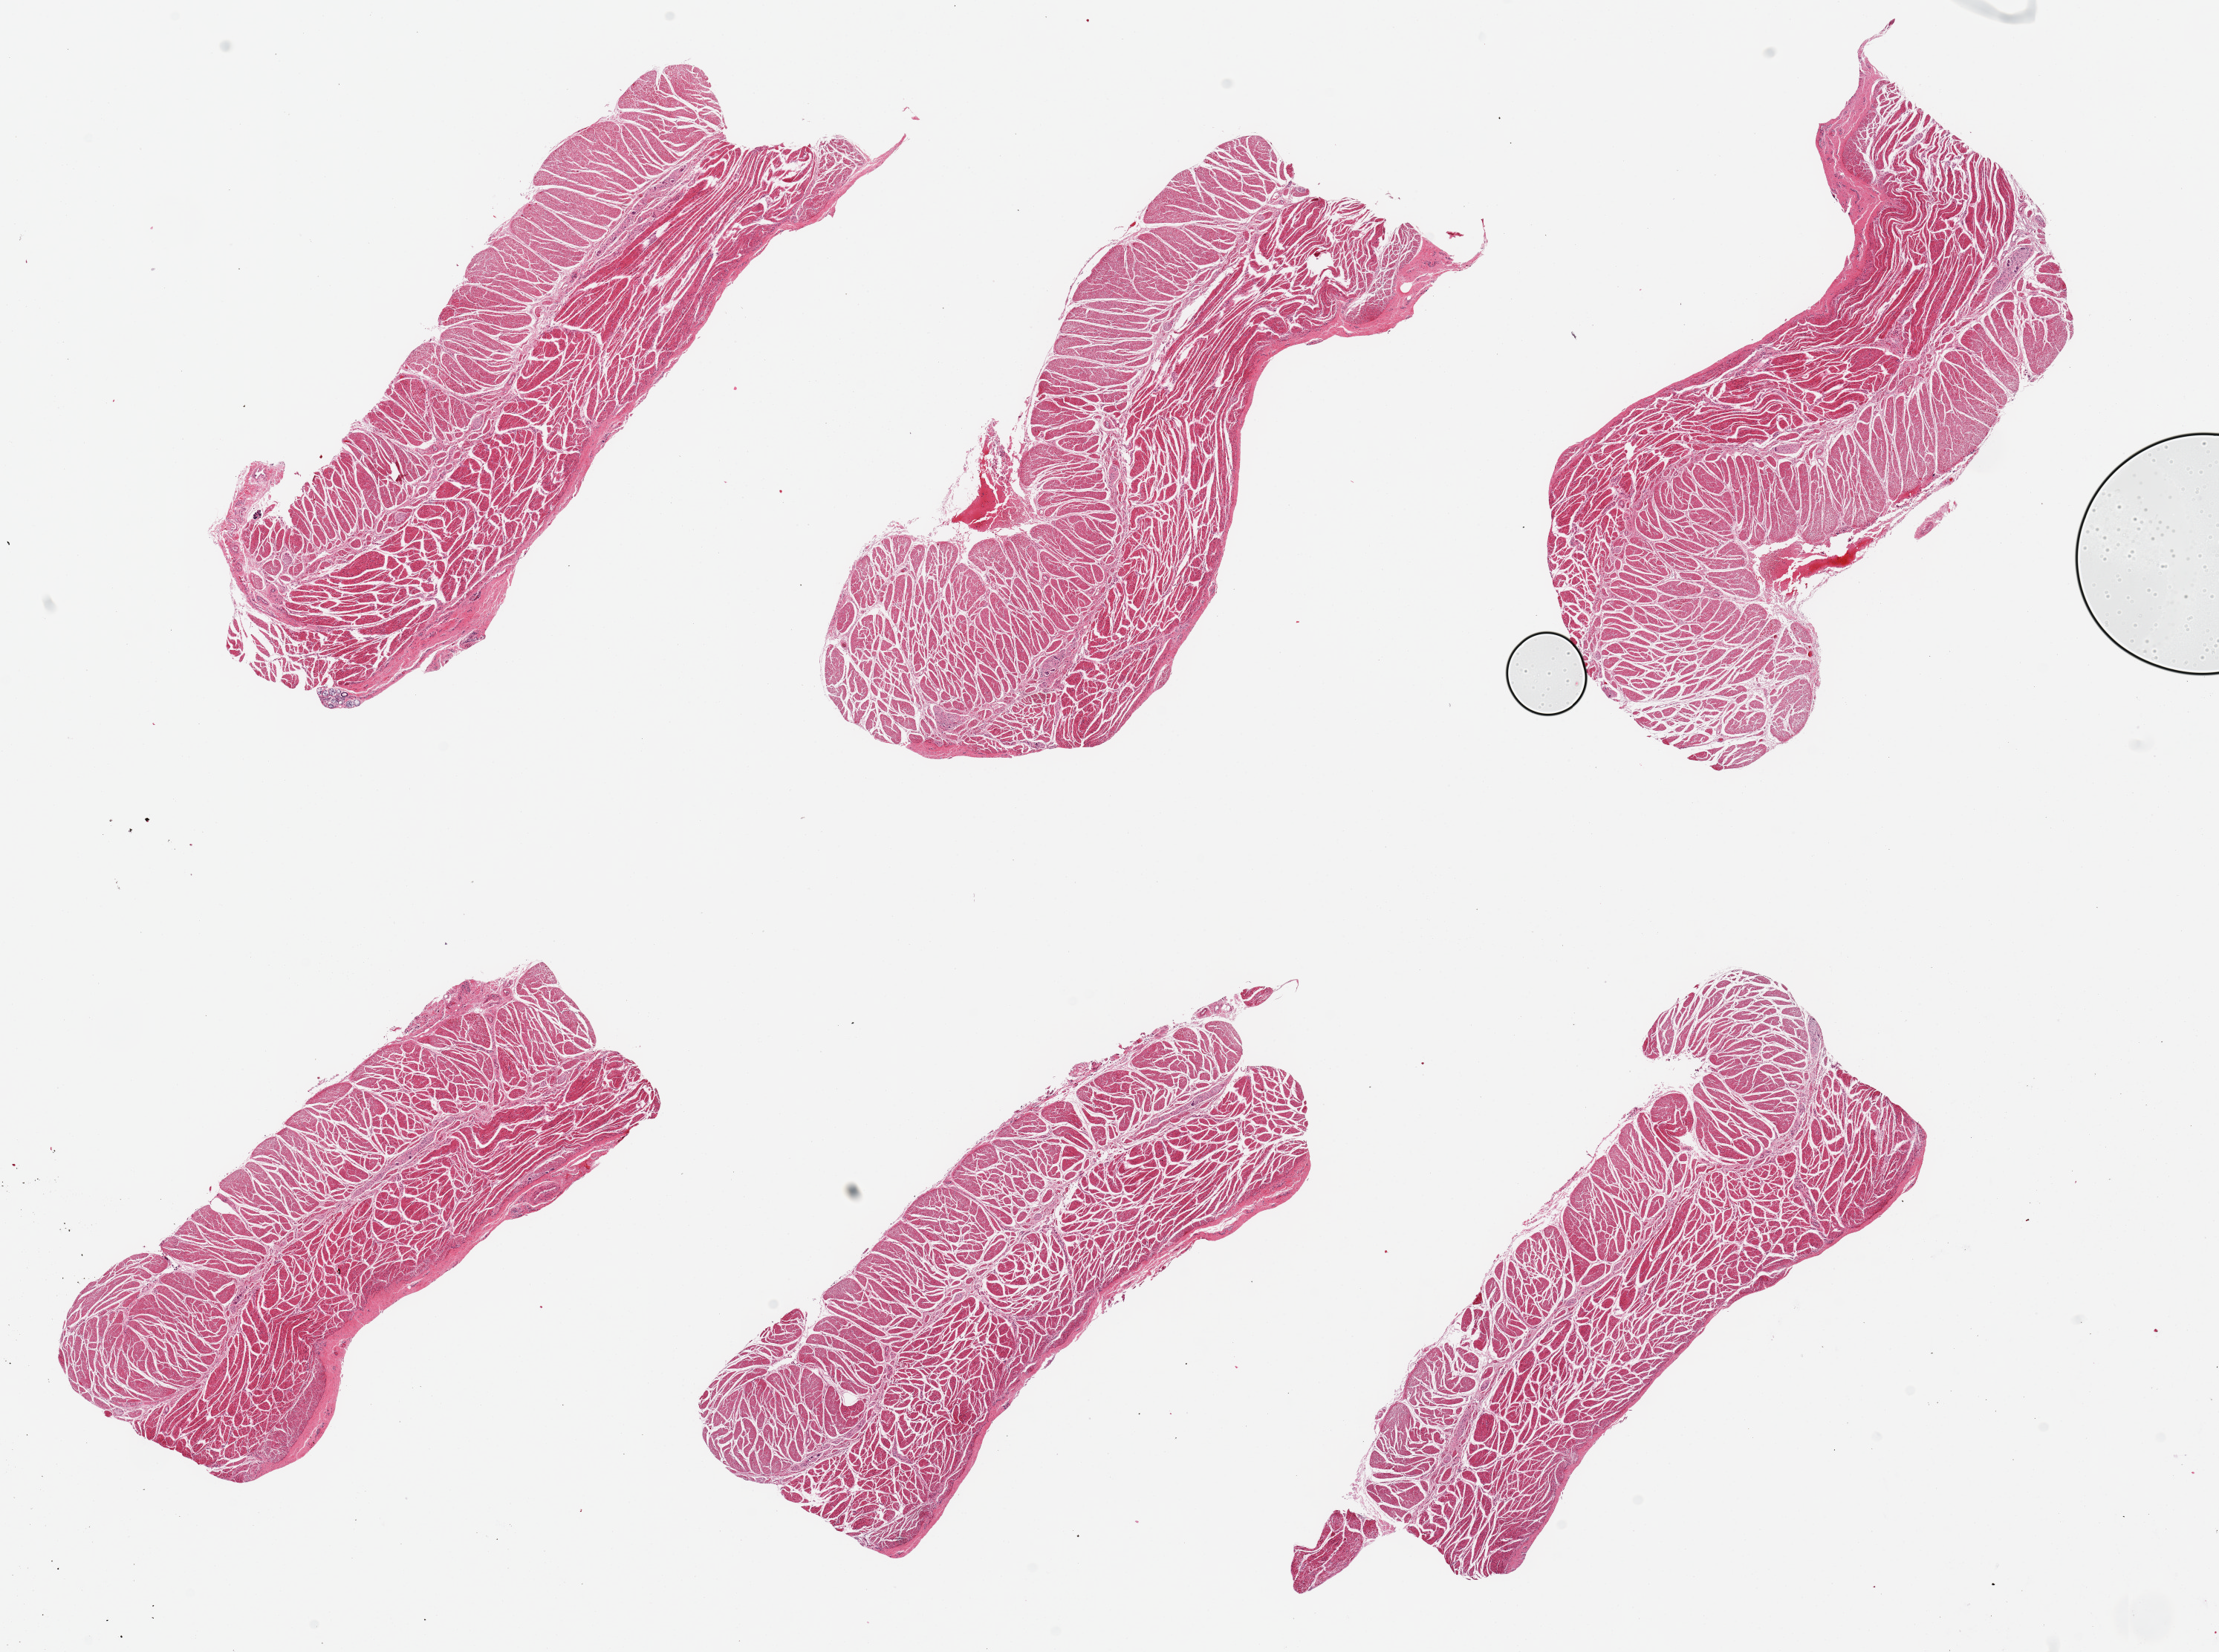
Whole-slide image, H&E stain, low-resolution overview of the scanned area, about 23.6 x 17.6 mm, PAXgene-fixed paraffin-embedded (PFPE) section, section of esophageal muscle (target tissue), donor tissue sample. Donor sex: male.
Reviewer comment on this tissue sample: 6 pieces, all muscularis; good specimens.